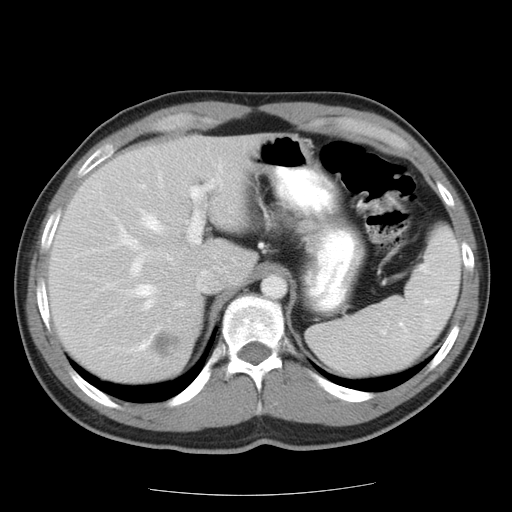
Contrast-enhanced abdominal CT, one axial slice; position 14 of 22 along the scan axis; intravenous contrast given; soft-tissue window (W 400 / L 40 HU); 7.5 mm slice thickness; 512 × 512 image matrix. Male patient, age 41 years. From the clinical record (not read from this slice): diagnosis: colorectal cancer liver metastases, imaged before liver resection; multiple liver metastases: no; largest metastasis: 2.7 cm; disease in both lobes: no.
Outlined on this slice (manually delineated by an expert):
- hepatic veins: bounding box [x1, y1, x2, y2] px = [137, 215, 162, 310]
- liver: [50, 138, 253, 381]
- planned liver remnant (the part of the liver to remain after resection): [50, 138, 254, 344]
- portal vein (with intrahepatic branches): [119, 186, 212, 277]
- liver metastasis: [147, 328, 185, 361]